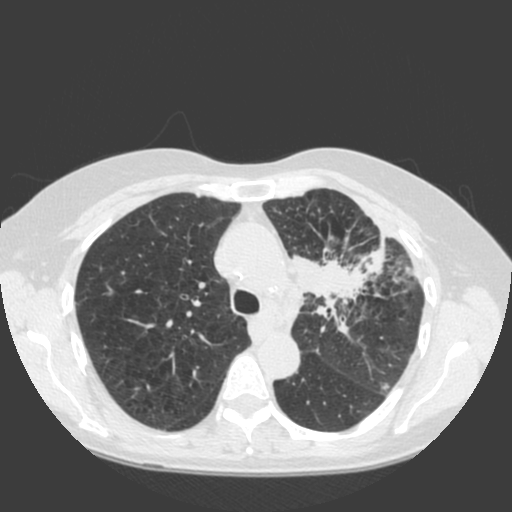
Low-dose screening chest CT, one axial slice; lung window (W 1500 / L -600 HU); 2 mm slice thickness; 512 × 512 image matrix, field of view 350 × 350 mm.
Annotated regions visible in this slice (manually delineated by an expert):
- lesion 1 (tumor, hilum of left lung): bounding box <290,237,386,318> (left, top, right, bottom; pixels)